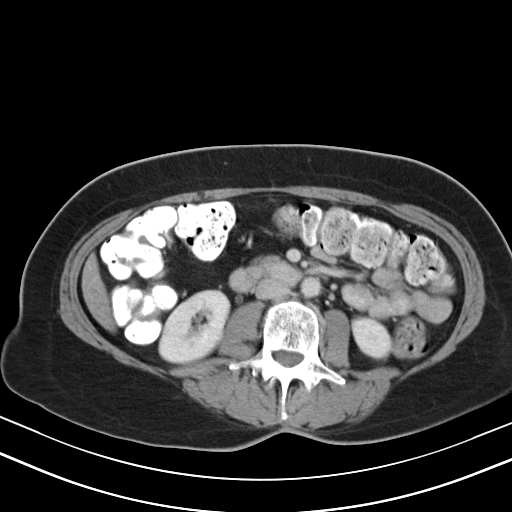
Contrast-enhanced abdominal CT, one axial slice. Position 14 of 47 along the scan axis. Reconstruction kernel B40s. 130 kVp. Intravenous contrast given. Soft-tissue window (W 400 / L 40 HU). 5 mm slice thickness. 512 × 512 image matrix, field of view 350 × 350 mm. Female patient. Case-level facts recorded for this patient, not image findings: diagnosis: colorectal cancer liver metastases, imaged before liver resection; multiple liver metastases: no; largest metastasis: 3.5 cm; chemotherapy before resection: yes.
Structures marked on this image (manually delineated by an expert):
- liver: bounding box <84,263,112,325> (left, top, right, bottom; pixels)
- planned liver remnant (the part of the liver to remain after resection): <84,263,112,324>